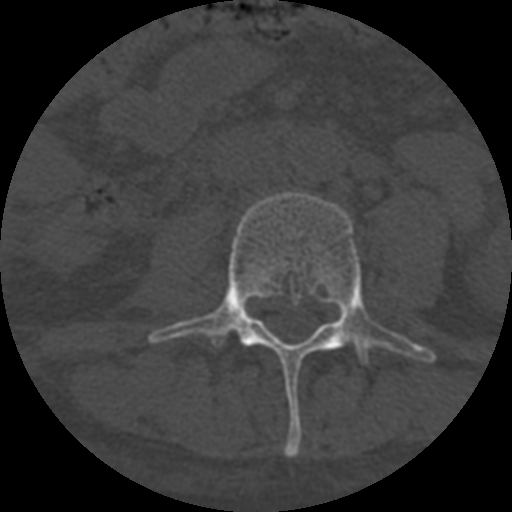
CT including the spine, one axial slice. Slice 234 of 708 in the series (ordered by position). 120 kVp. One of 3 acquisitions stored at this slice position. Bone window (W 1800 / L 400 HU). 1.25 mm slice thickness. 512 × 512 image matrix. Patient age 55 years. From the clinical record (not read from this slice): primary cancer: colon; vertebrae with lytic lesions (as recorded): T12, L1, L5.
Annotated regions visible in this slice (semi-automatic segmentation, software-assisted and operator-edited):
- L3 vertebra: bounding box [x1, y1, x2, y2] px = [148, 191, 437, 457]